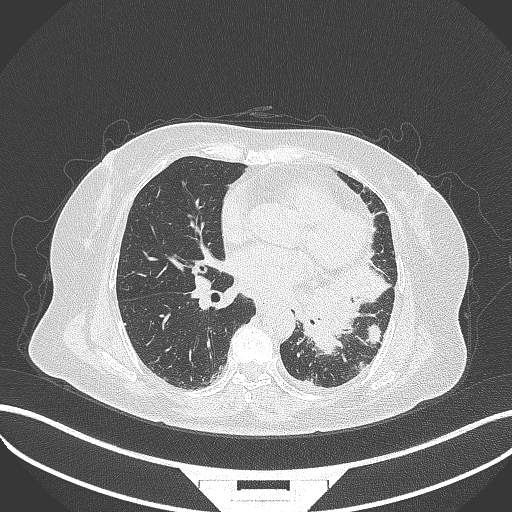
Chest CT, one axial slice. Reconstruction kernel B70f. 120 kVp. Lung window (W 1500 / L -600 HU). 1 mm slice thickness. 512 × 512 image matrix, field of view 400 × 400 mm. Female patient, age 69 years. Case-level facts recorded for this patient, not image findings: clinical TNM (as recorded): T2b N3 M1.
Outlined on this slice (rectangle marked by the reading radiologist):
- lung tumour (recorded histology: adenocarcinoma): box from (x=301, y=257) to (x=390, y=357) px